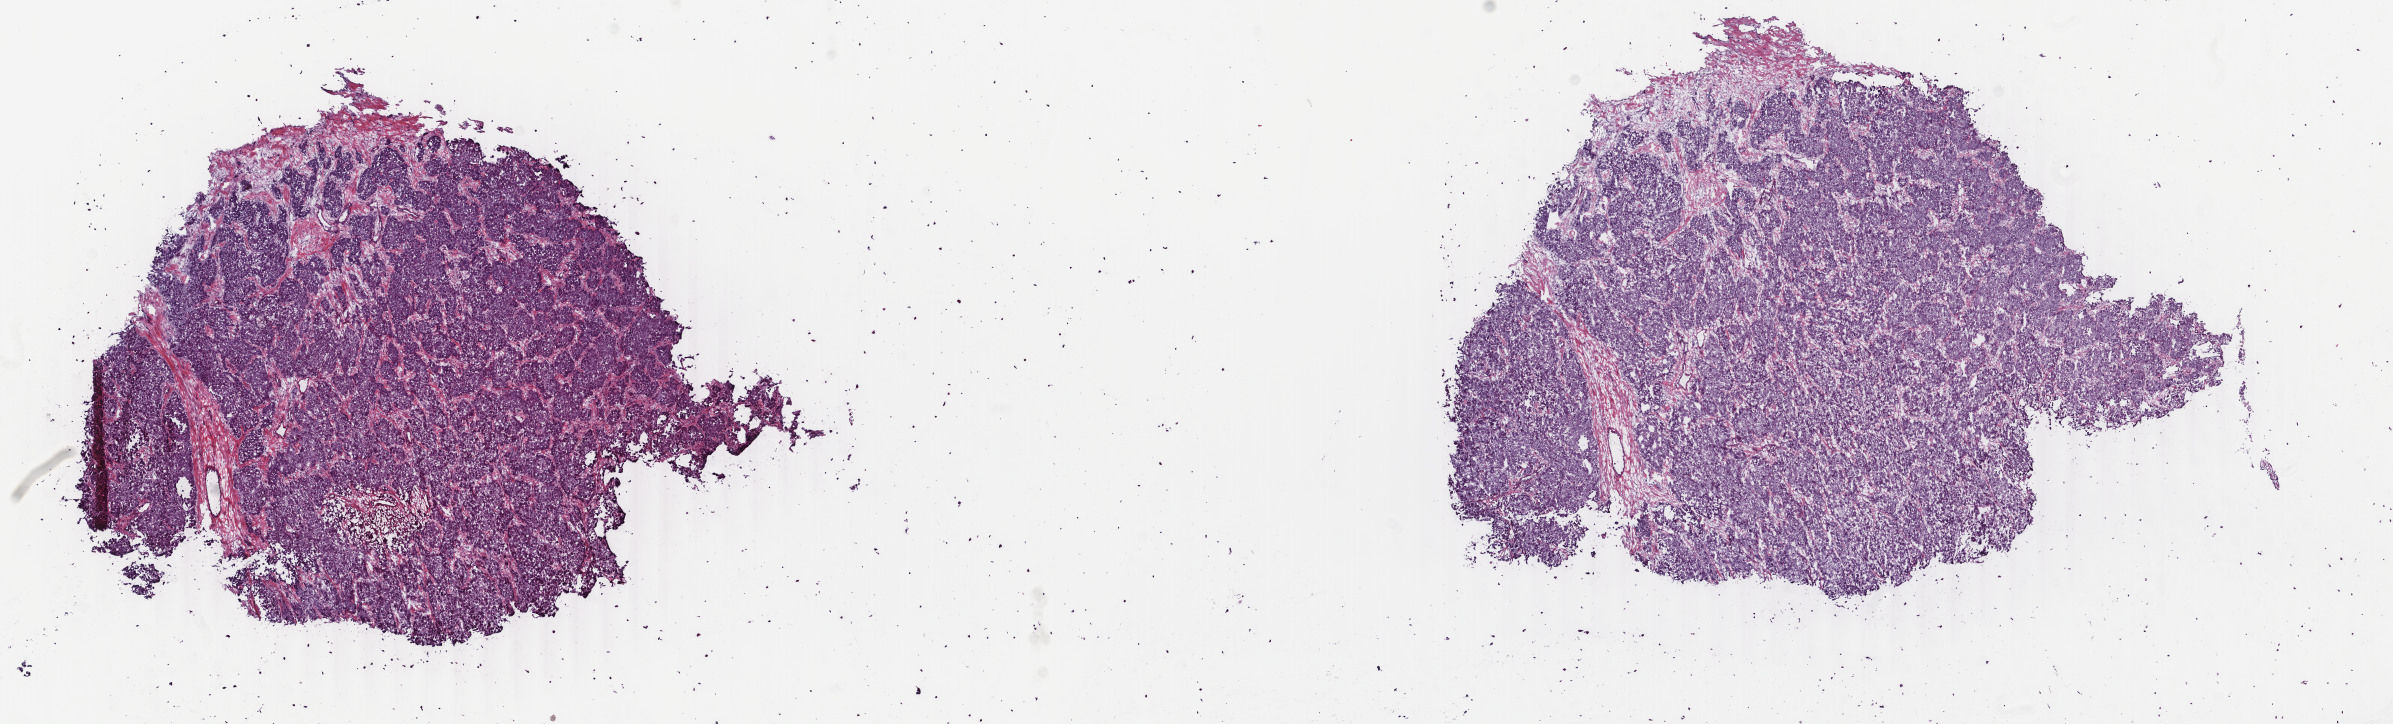
H&E whole-slide image — whole scanned area (about 19.0 x 5.8 mm, slide scanned at 40x) shown as a low-resolution overview. Frozen section from the bottom of the tissue portion. Sample: primary tumour, liver. Female, age 66 years at initial diagnosis. Histologic grade: G2 (moderately differentiated). Slide review estimates, as recorded: tumour cells 95%, tumour nuclei 95%, normal cells 0%, stromal cells 5%, necrosis 0%. Infiltration values recorded for this section: lymphocyte infiltration 0%, monocyte infiltration 0%, neutrophil infiltration 0%.
Histologic diagnosis: Hepatocellular carcinoma, NOS.